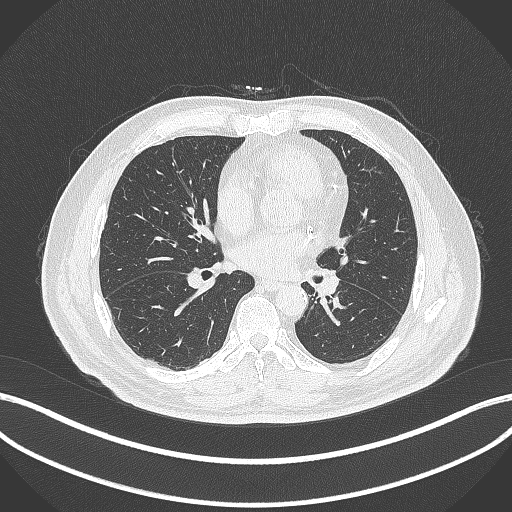
Chest CT, one axial slice; slice 132 of 312 in the series (ordered by position); lung window (W 1500 / L -600 HU); 1 mm slice thickness; 512 × 512 image matrix, field of view 400 × 400 mm. Male patient, age 71 years. Case-level facts recorded for this patient, not image findings: clinical TNM (as recorded): T1b N0 M0.
Structures marked on this image (rectangle marked by the reading radiologist):
- lung tumour (recorded histology: squamous cell carcinoma): bounding box (x1, y1, x2, y2) in pixels: (314, 269, 340, 298)